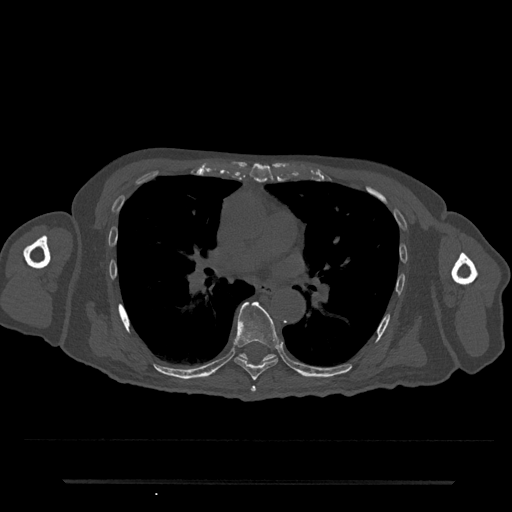
CT including the spine, one axial slice; slice 467 of 797 in the series (ordered by position); reconstruction kernel Br40s/3; 120 kVp; bone window (W 1800 / L 400 HU); 512 × 512 image matrix. Patient: male, 74 years. From the clinical record (not read from this slice): primary cancer: prostate.
Outlined on this slice (semi-automatically segmented with operator editing):
- T6 vertebra: bounding box (x1, y1, x2, y2) in pixels: (251, 386, 256, 392)
- T7 vertebra: (234, 301, 279, 381)
- T8 vertebra: (239, 353, 276, 362)